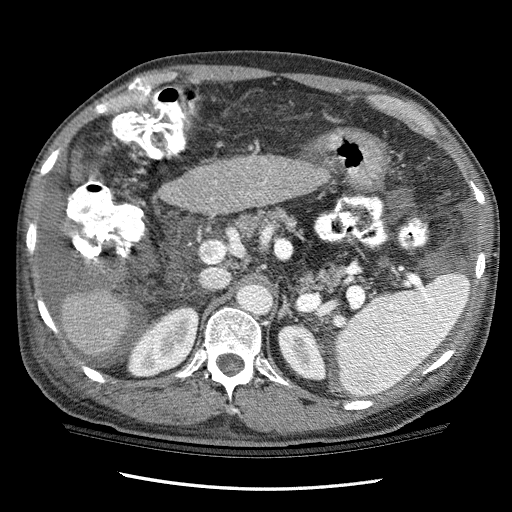
Contrast-enhanced abdominal CT (liver protocol), one axial slice. Slice 58 of 114 in the series (ordered by position). One of 3 acquisitions stored at this slice position. Soft-tissue window (W 400 / L 40 HU). 2.5 mm slice thickness. 512 × 512 image matrix. Case-level facts recorded for this patient, not image findings: diagnosis: hepatocellular carcinoma (patient treated with transarterial chemoembolisation; whether this scan precedes or follows treatment is not stated here); TNM stage (as recorded): Stage-I; Child-Pugh class: C; tumour differentiation: well differentiated.
Structures marked on this image (semi-automatic segmentation, software-assisted and operator-edited):
- liver parenchyma outside the tumour (the mass and vessels are separate outlines, so this box may not span the whole liver): bounding box [x1, y1, x2, y2] px = [62, 158, 328, 356]